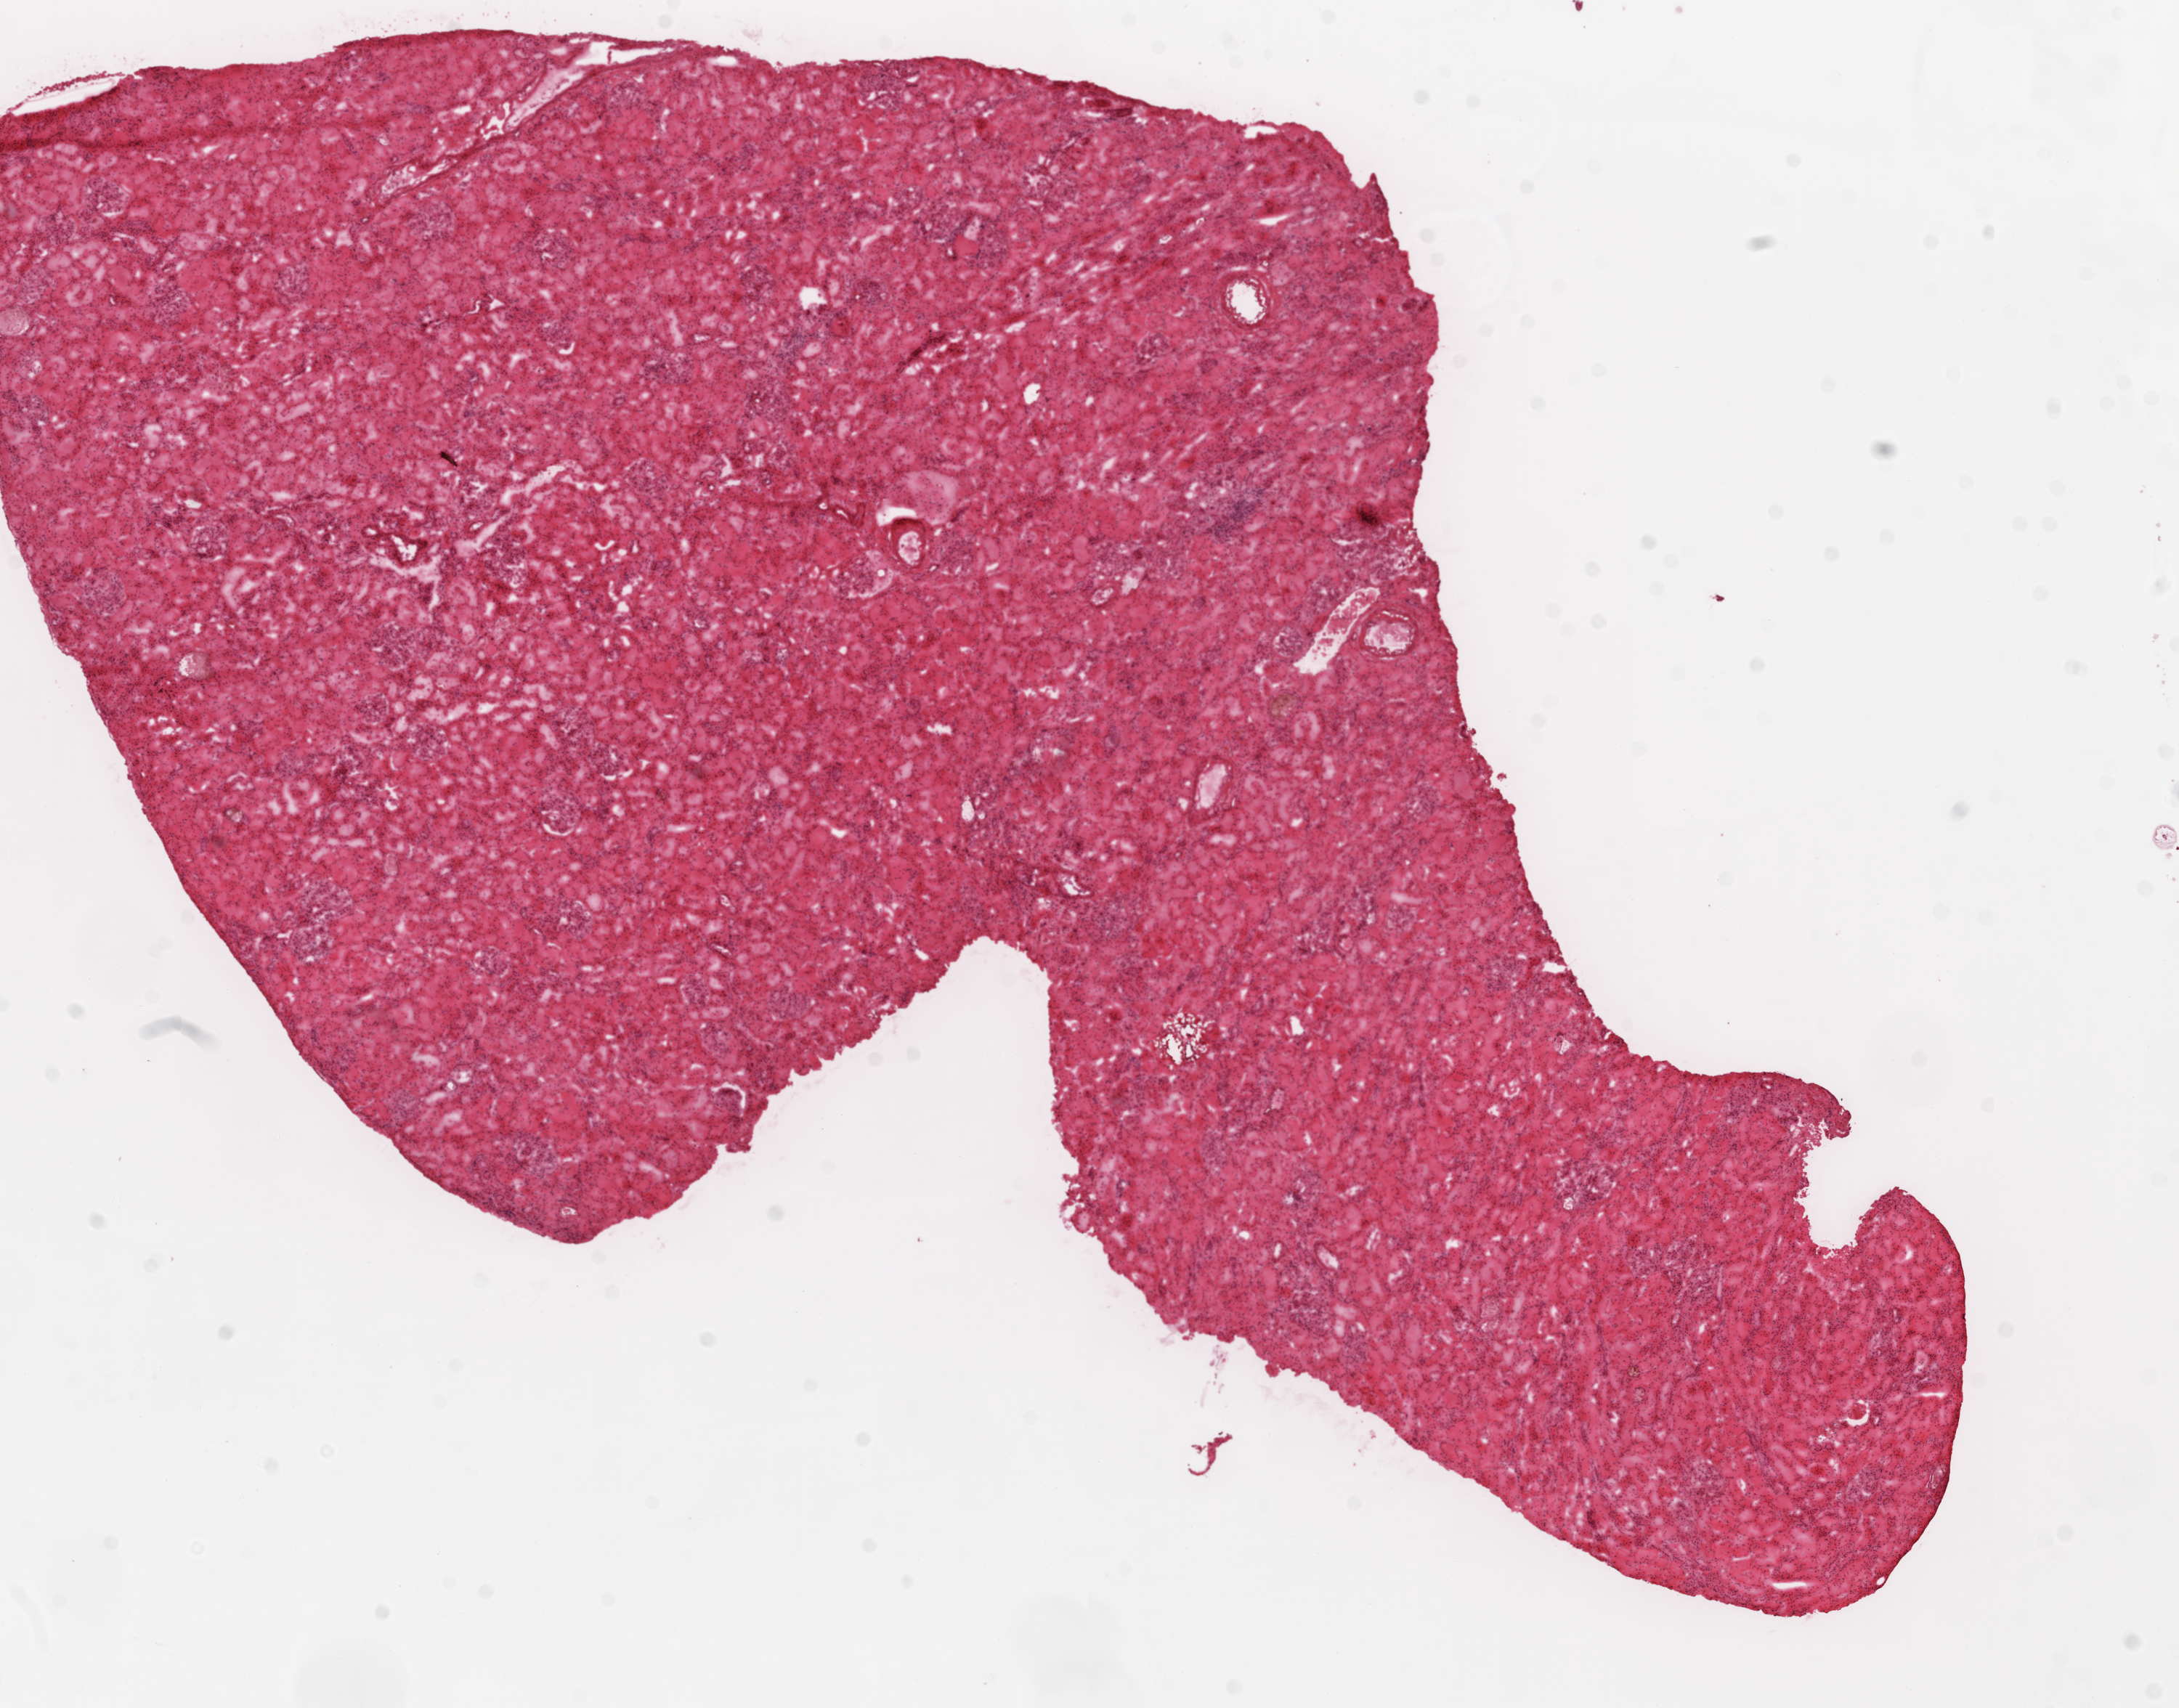
Whole-slide histology image, Hematoxylin and eosin (H&E) stained, shown as a low-resolution overview of the whole scanned area (about 12.0 x 9.4 mm); frozen section from the top of the tissue portion; sample: solid tissue normal (non-tumour tissue), kidney. Patient: female, age at initial diagnosis 43 years.
This section: solid tissue normal sample (biorepository sample class). Patient diagnosis: Clear cell adenocarcinoma, NOS.